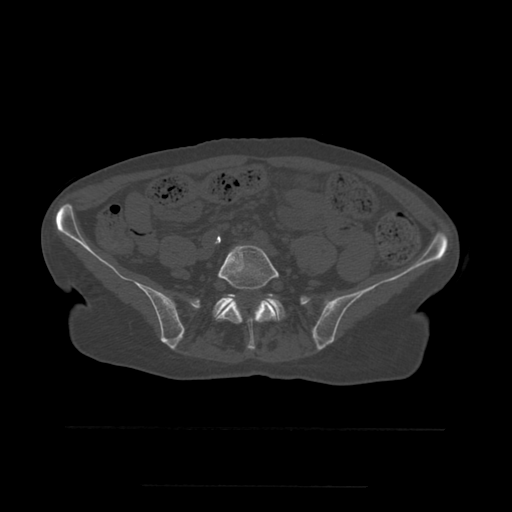
CT including the spine, one axial slice. Slice 141 of 544 in the series (ordered by position). Bone window (W 1800 / L 400 HU). 512 × 512 image matrix, field of view 350 × 350 mm. Patient age 58 years. Case-level facts recorded for this patient, not image findings: primary cancer: lung.
Structures marked on this image (semi-automatically segmented with operator editing):
- L5 vertebra: bounding box [x1, y1, x2, y2] px = [217, 246, 279, 350]